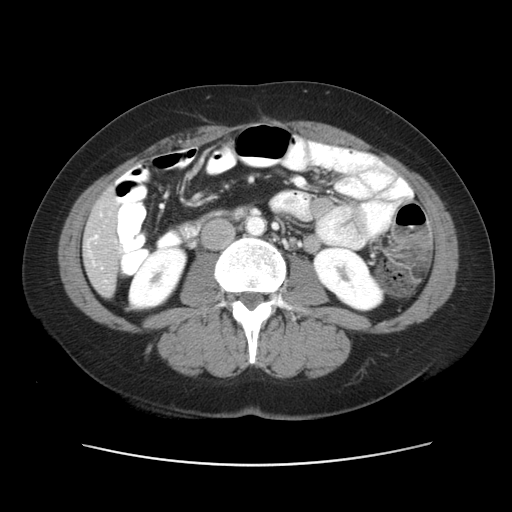
Contrast-enhanced abdominal CT, one axial slice; position 15 of 52 along the scan axis; reconstruction kernel STANDARD; 120 kVp; soft-tissue window (W 400 / L 40 HU); 5 mm slice thickness; 512 × 512 image matrix. Female patient, age 48 years. From the clinical record (not read from this slice): diagnosis: colorectal cancer liver metastases, imaged before liver resection; multiple liver metastases: yes; largest metastasis: 4.5 cm; disease in both lobes: yes.
Structures marked on this image (manually delineated by an expert):
- hepatic veins: bounding box (x1, y1, x2, y2) in pixels: (88, 214, 102, 269)
- liver: (84, 193, 120, 294)